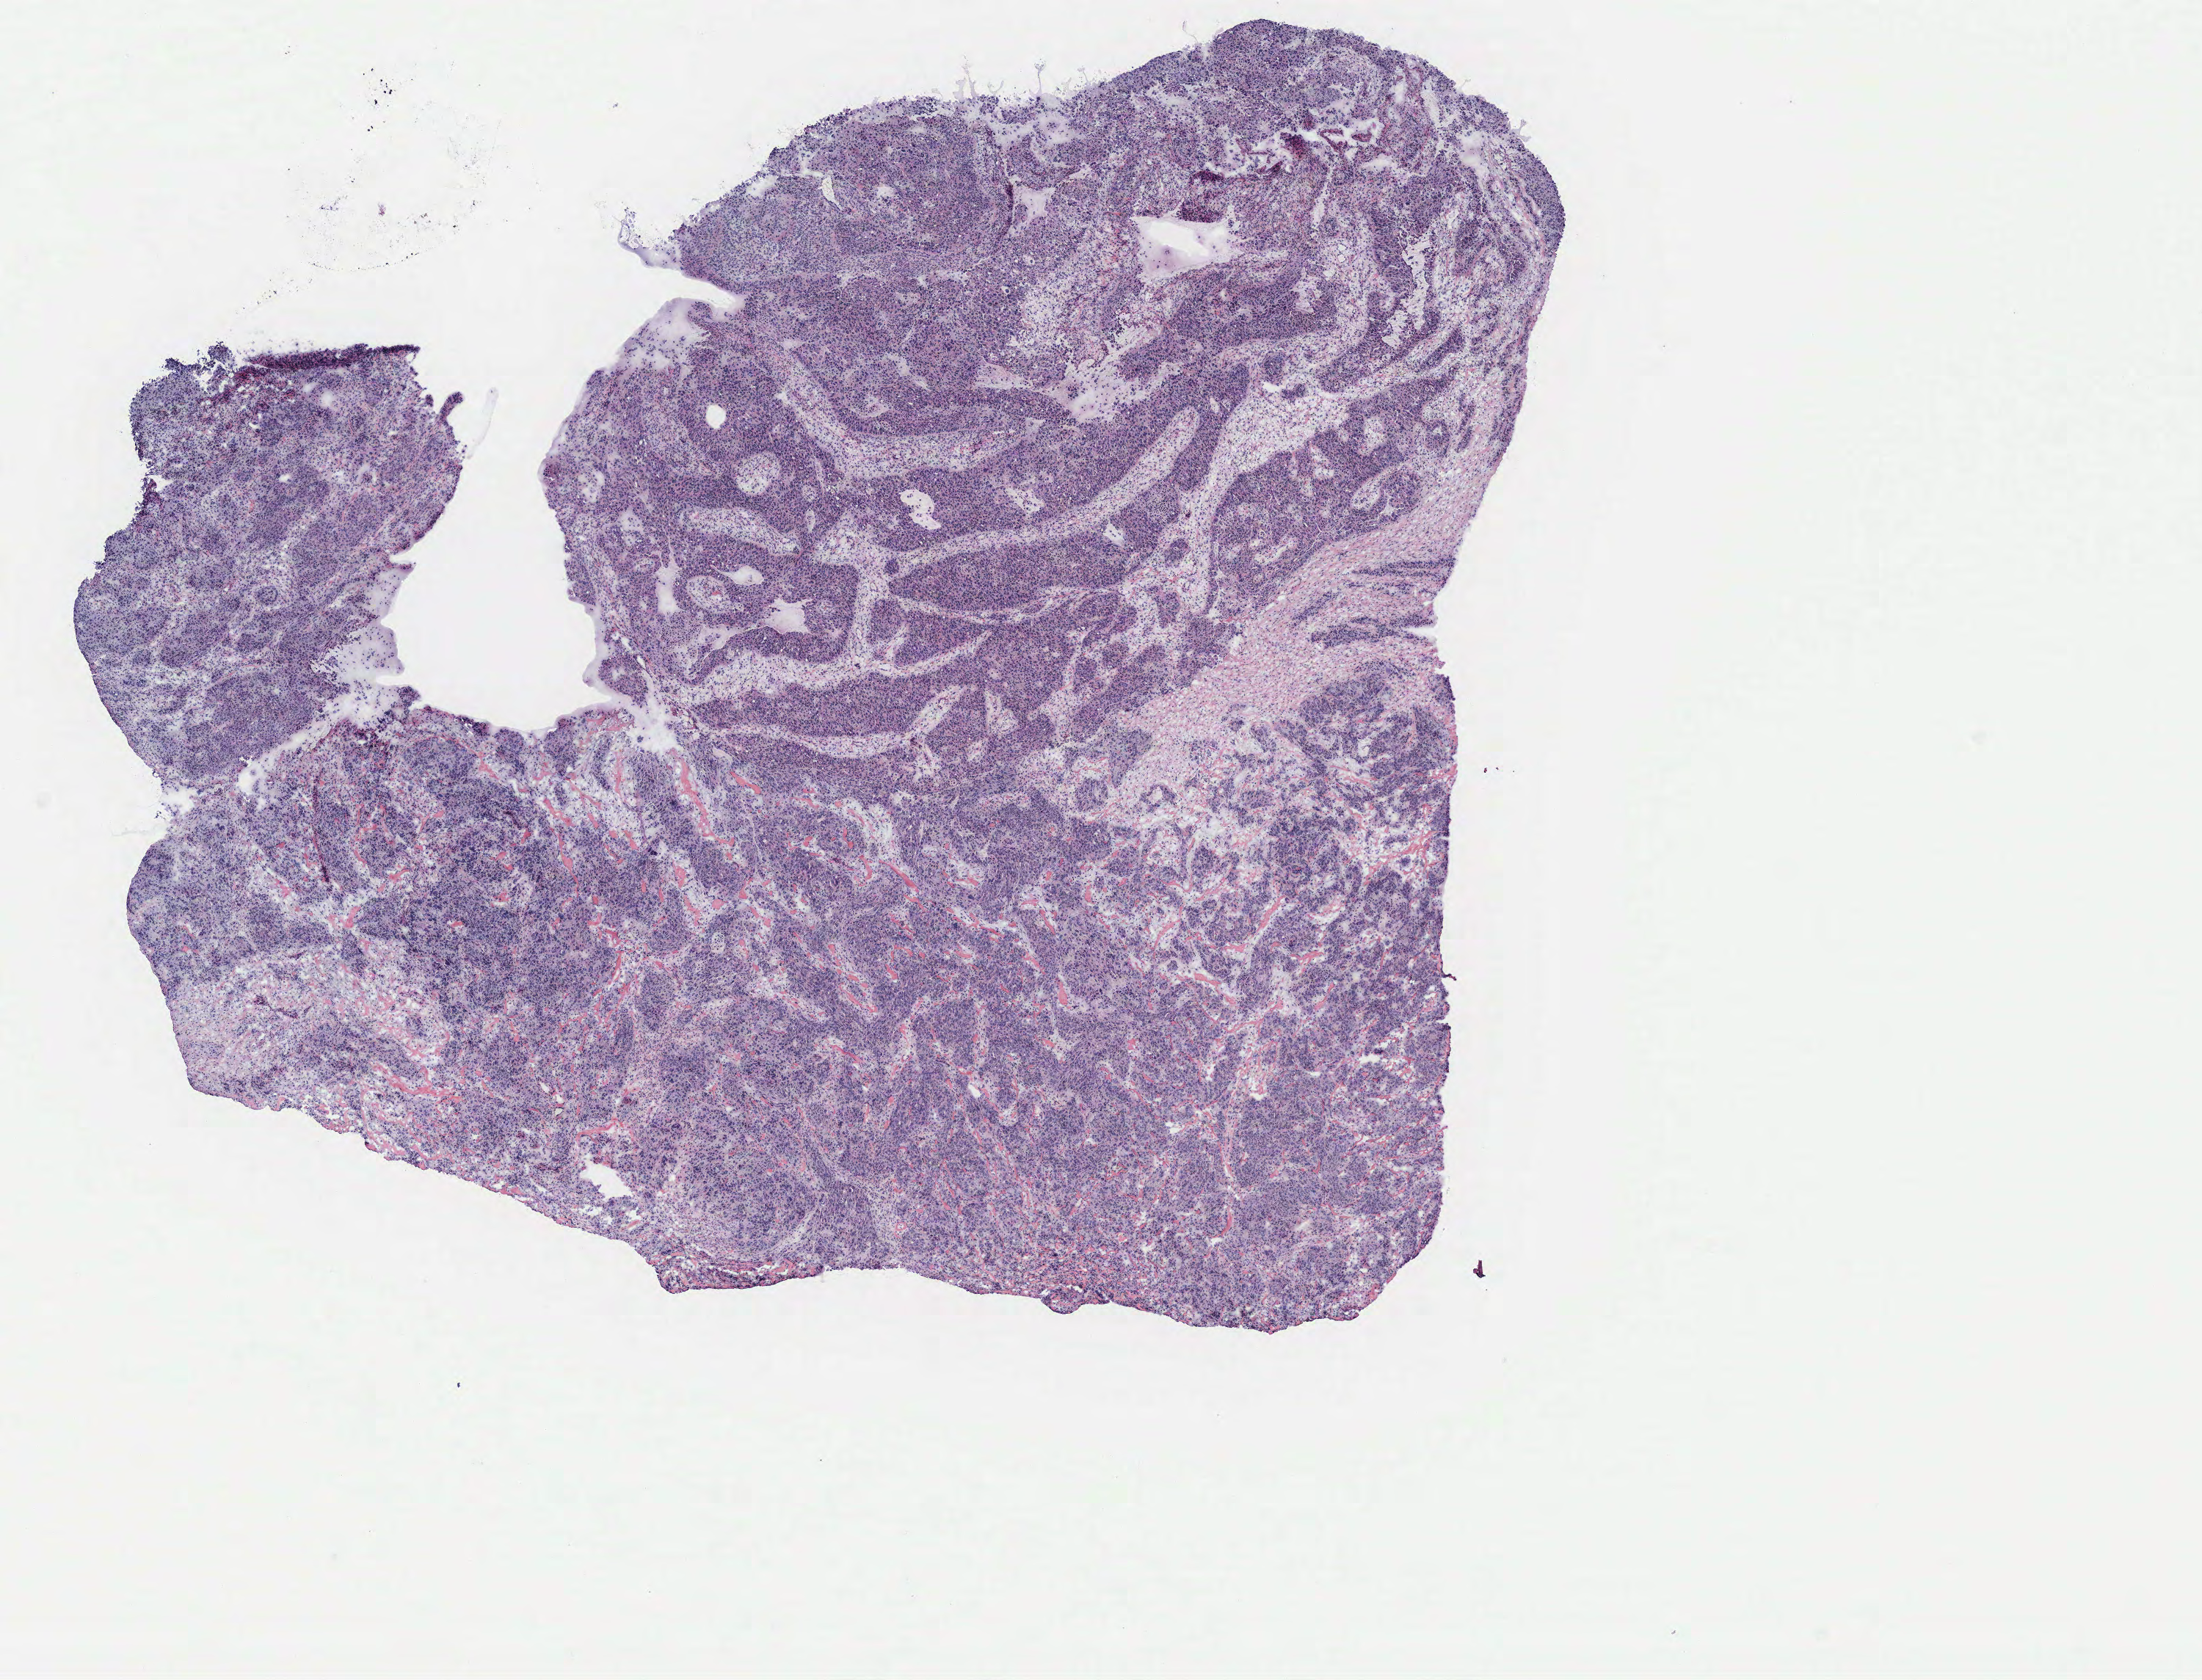
H&E whole-slide image, low-resolution overview of the scanned area, about 12.0 x 9.2 mm. Ovary, tissue type not recorded. Patient sex: female.
Patient diagnosis: Serous adenocarcinoma, NOS.